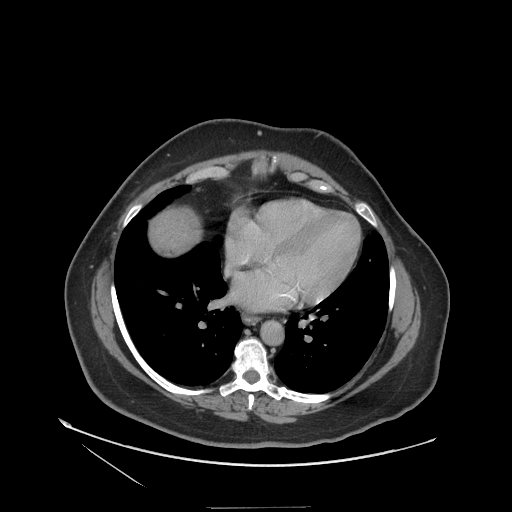
Contrast-enhanced abdominal CT (liver protocol), one axial slice. Slice 112 of 127 in the series (ordered by position). Reconstruction kernel STANDARD. 140 kVp. Soft-tissue window (W 400 / L 40 HU). 512 × 512 image matrix, field of view 480 × 480 mm. From the clinical record (not read from this slice): diagnosis: hepatocellular carcinoma (patient treated with transarterial chemoembolisation; whether this scan precedes or follows treatment is not stated here); TNM stage (as recorded): Stage-II; Child-Pugh class: A; tumour differentiation: well differentiated; tumour size: 3 cm.
Structures marked on this image (semi-automatic segmentation, software-assisted and operator-edited):
- liver parenchyma outside the tumour (the mass and vessels are separate outlines, so this box may not span the whole liver): bounding box <150,210,196,252> (left, top, right, bottom; pixels)